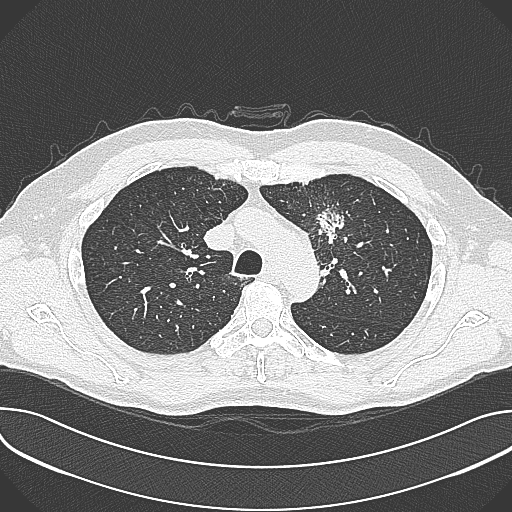
Chest CT (low-dose screening protocol), one axial image; baseline screening round; lung window (W 1500 / L -600 HU); 1 mm slice thickness; lung (sharp) reconstruction kernel (B80f); 512 × 512 image matrix. Male participant, aged 59 years at enrolment. Current smoker at enrolment.
Lesion marked by an expert reader, bounding box (x1, y1, x2, y2) in pixels: (301, 200, 358, 257). The screening reader recorded 2 non-calcified nodules or masses ≥4 mm on this exam (left upper lobe, left upper lobe); which of them this box marks is not recorded. Lung cancer was diagnosed 21 days after this screen: non-small cell carcinoma, left upper lobe, poorly differentiated (G3), stage IIIA (AJCC 6th edition), 35 mm at pathology.